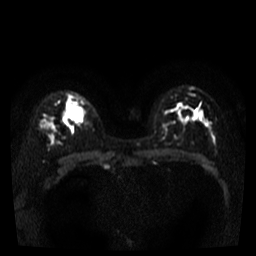
Breast MRI, one axial slice. Position 27 of 40 along the scan axis. Diffusion-weighted series; image 2 of 4 stored at this slice position (different b-values; order by instance number). 3 T. 5 mm slice thickness. 256 × 256 image matrix, field of view 280 × 280 mm. Female patient.
Annotated regions visible in this slice (expert manual segmentation):
- tumour on diffusion-weighted imaging: bounding box [x1, y1, x2, y2] px = [69, 108, 82, 120]